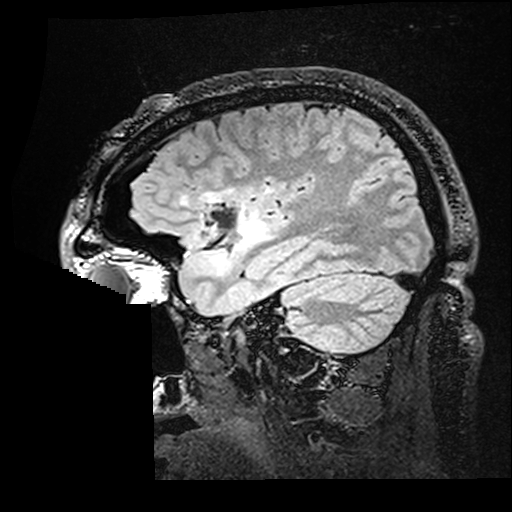
Brain MRI from a brain-tumour surgery series, one sagittal slice. Position 124 of 176 along the scan axis. T2 FLAIR. 1 mm slice thickness. 512 × 512 image matrix, field of view 250 × 250 mm. Case-level facts recorded for this patient, not image findings: histopathology: Astrocytoma; WHO grade: 2; IDH mutation: yes; tumour location: Right Insular.
Structures marked on this image (manually delineated by an expert):
- residual tumour: box from (x=182, y=192) to (x=267, y=252) px